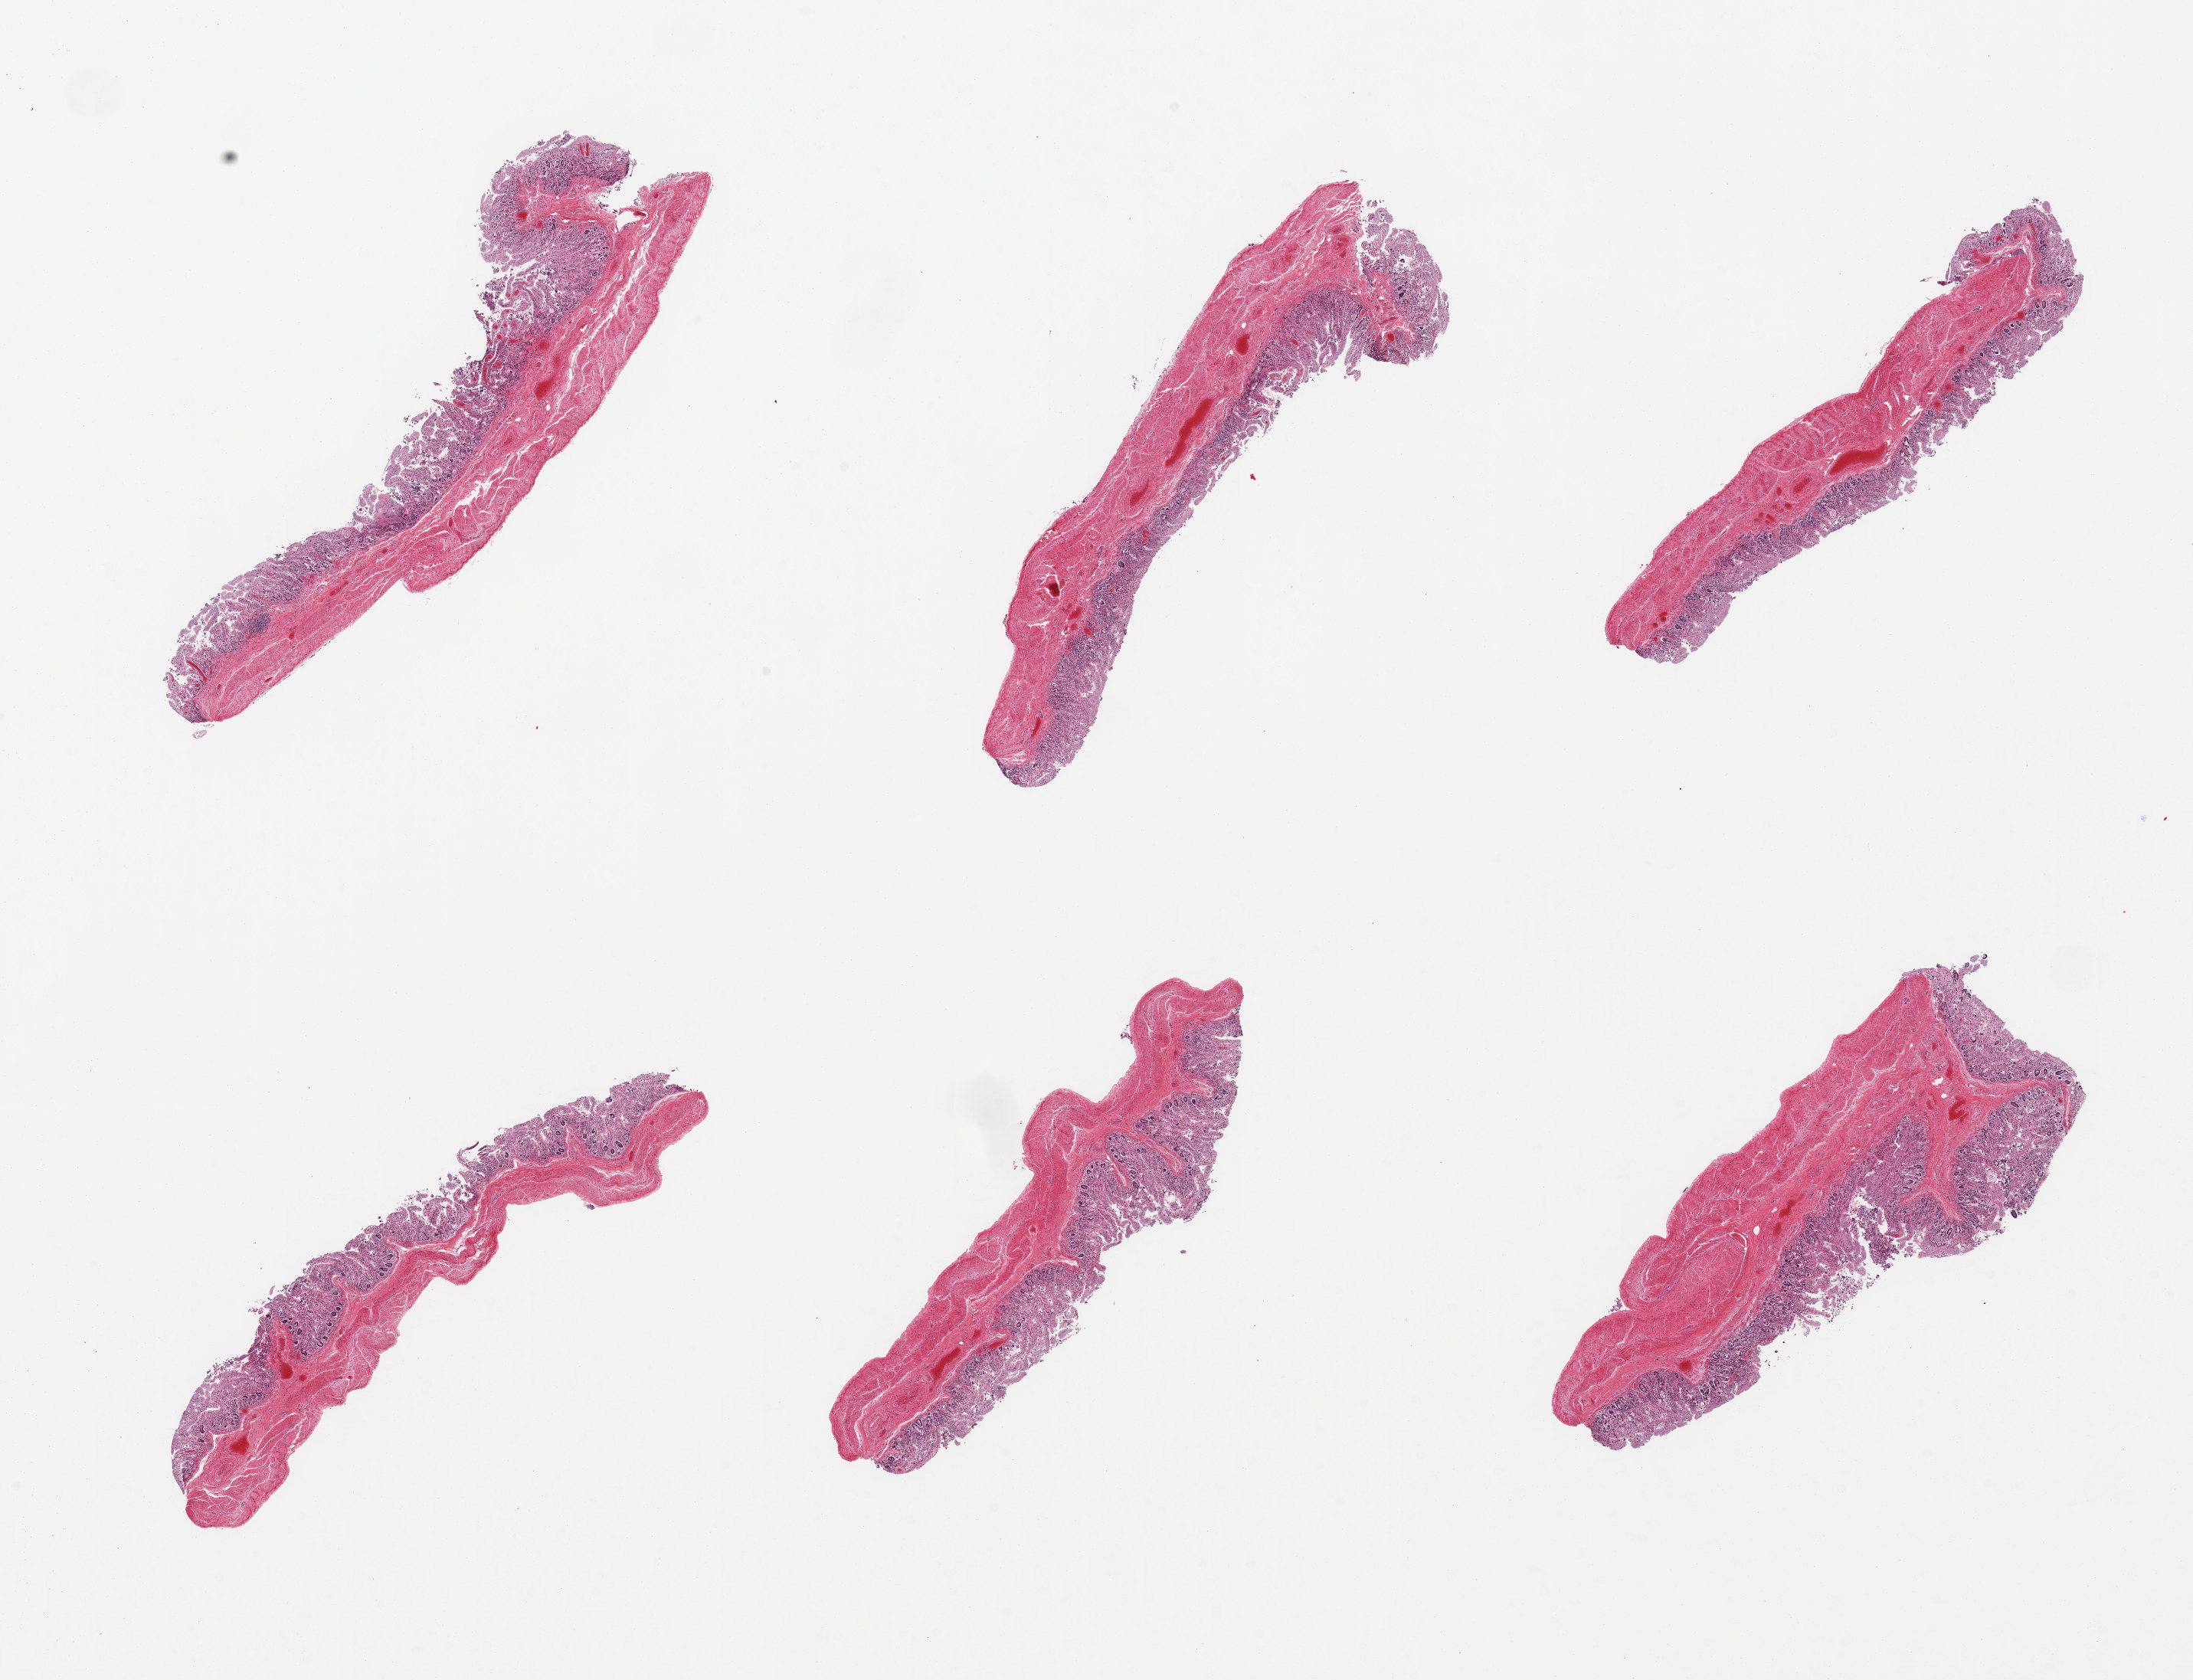
Hematoxylin and eosin (H&E) whole-slide image, brightfield — shown as a low-resolution overview of the whole scanned area (about 22.6 x 17.3 mm, from a 20x scan); PAXgene-fixed paraffin-embedded (PFPE) section; target tissue: transverse colon; tissue donor sample. Male donor.
Pathologist's review note for this sample: 6 pieces, mucosa ~0.4mm, ~30% thickness, advanced glandular autolysis.